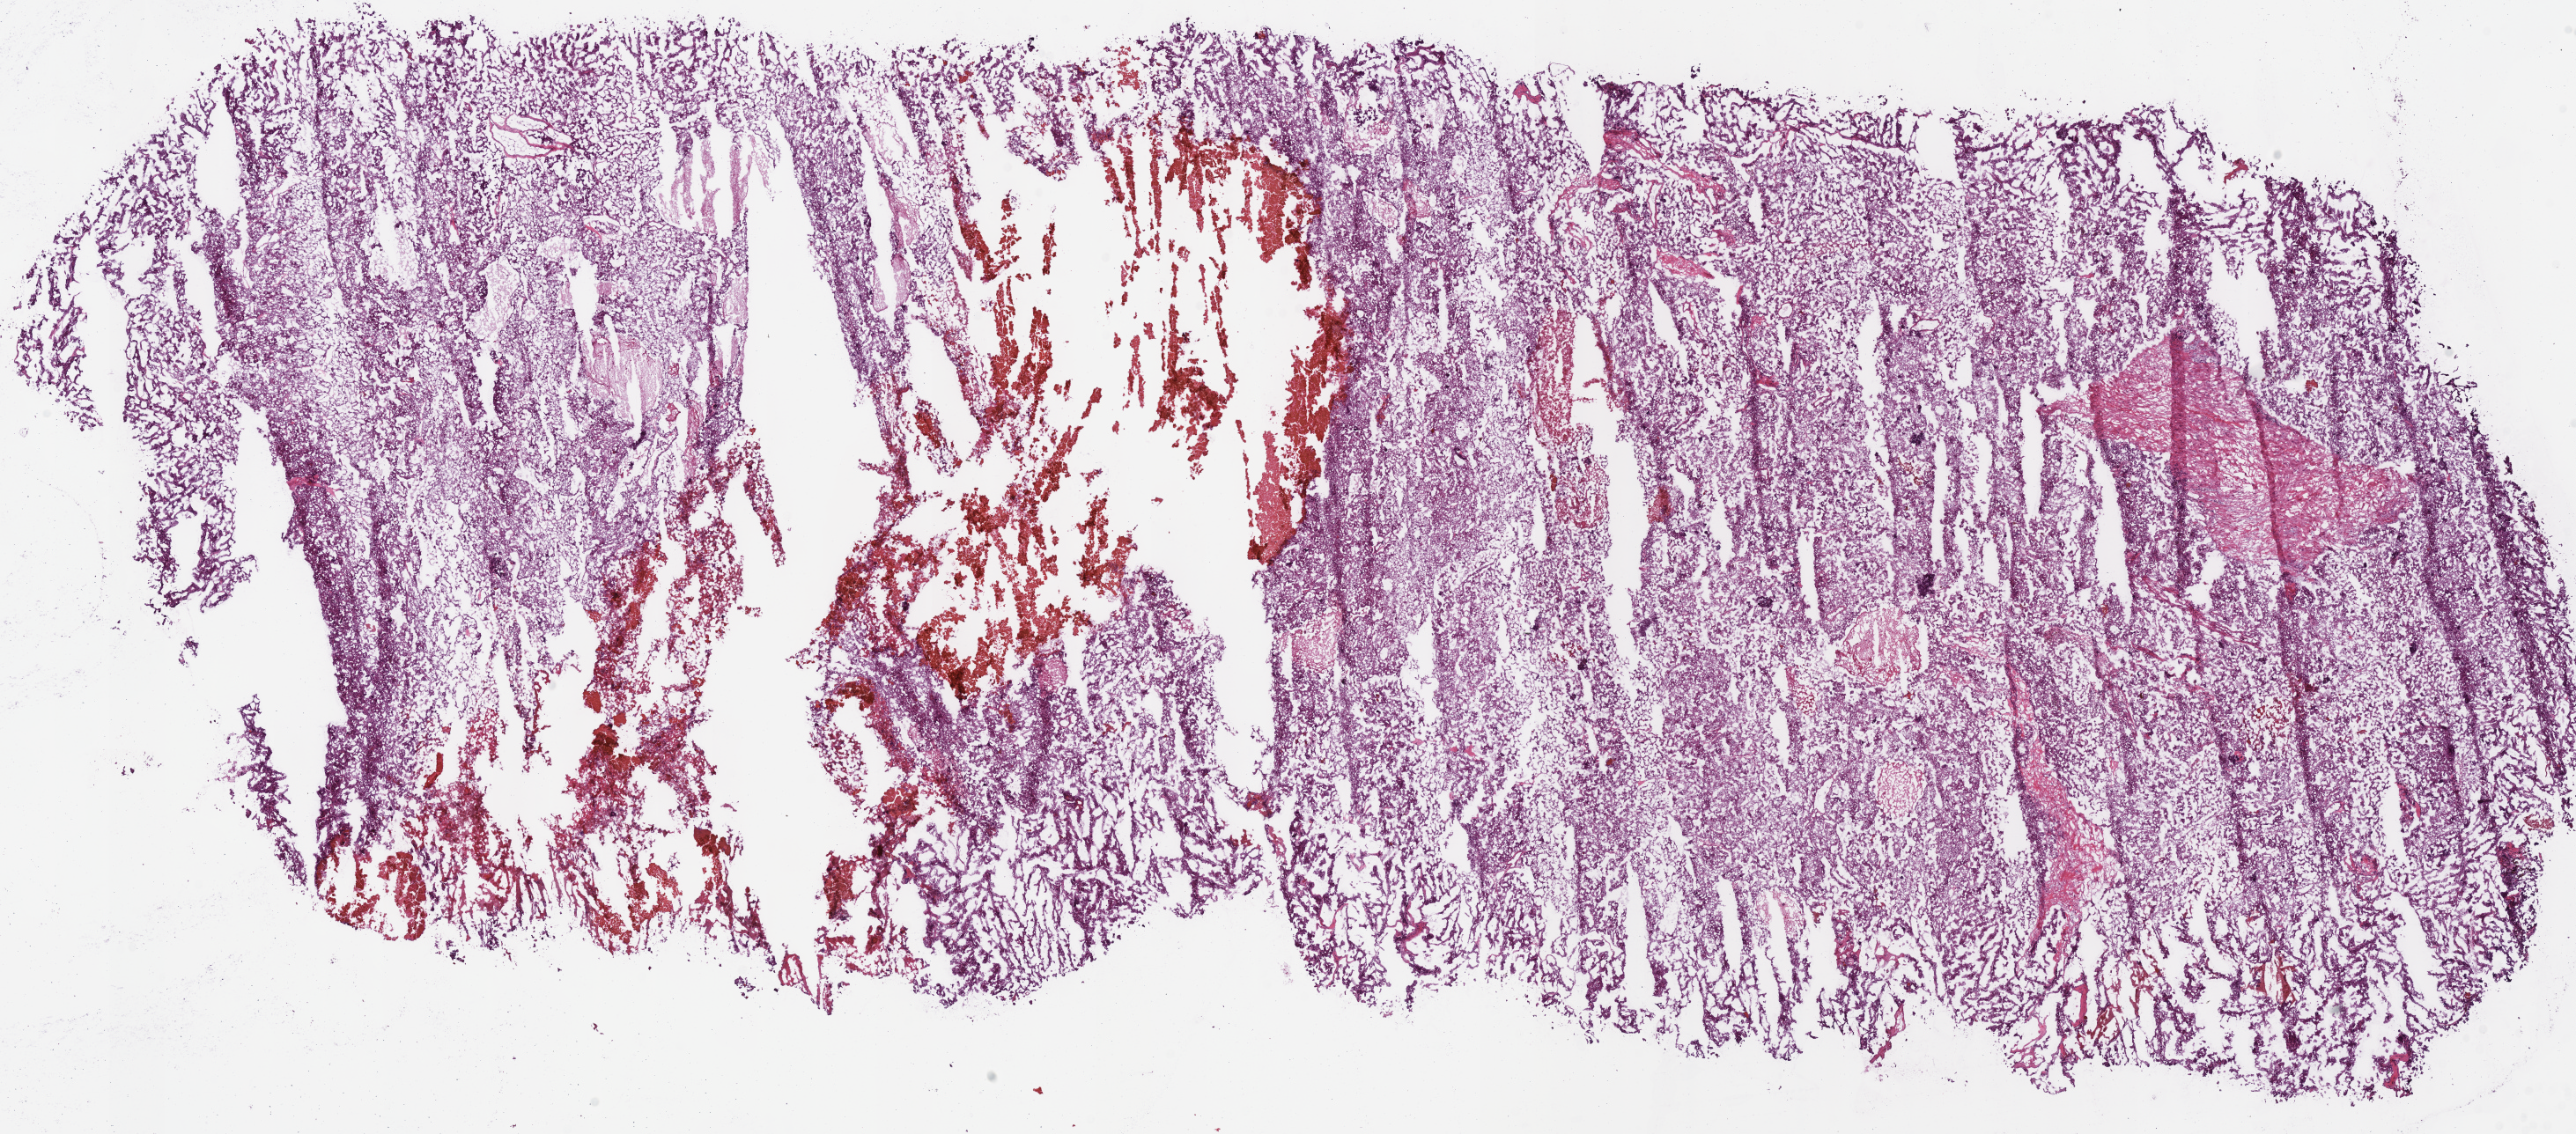
H&E-stained whole-slide image — whole scanned area (about 23.0 x 10.1 mm, from a 40x scan) shown as a low-resolution overview; frozen section; primary tumour sample from the kidney. Patient: male, age at initial diagnosis 41 years. Composition of this section per pathologist review: tumour cells 75%, tumour nuclei 90%, normal cells 0%, stromal cells 10%, necrosis 15%.
Histologic diagnosis: Renal cell carcinoma, chromophobe type. Laterality: right. TNM: T3a N0 M0. AJCC pathologic stage: III (7th edition).